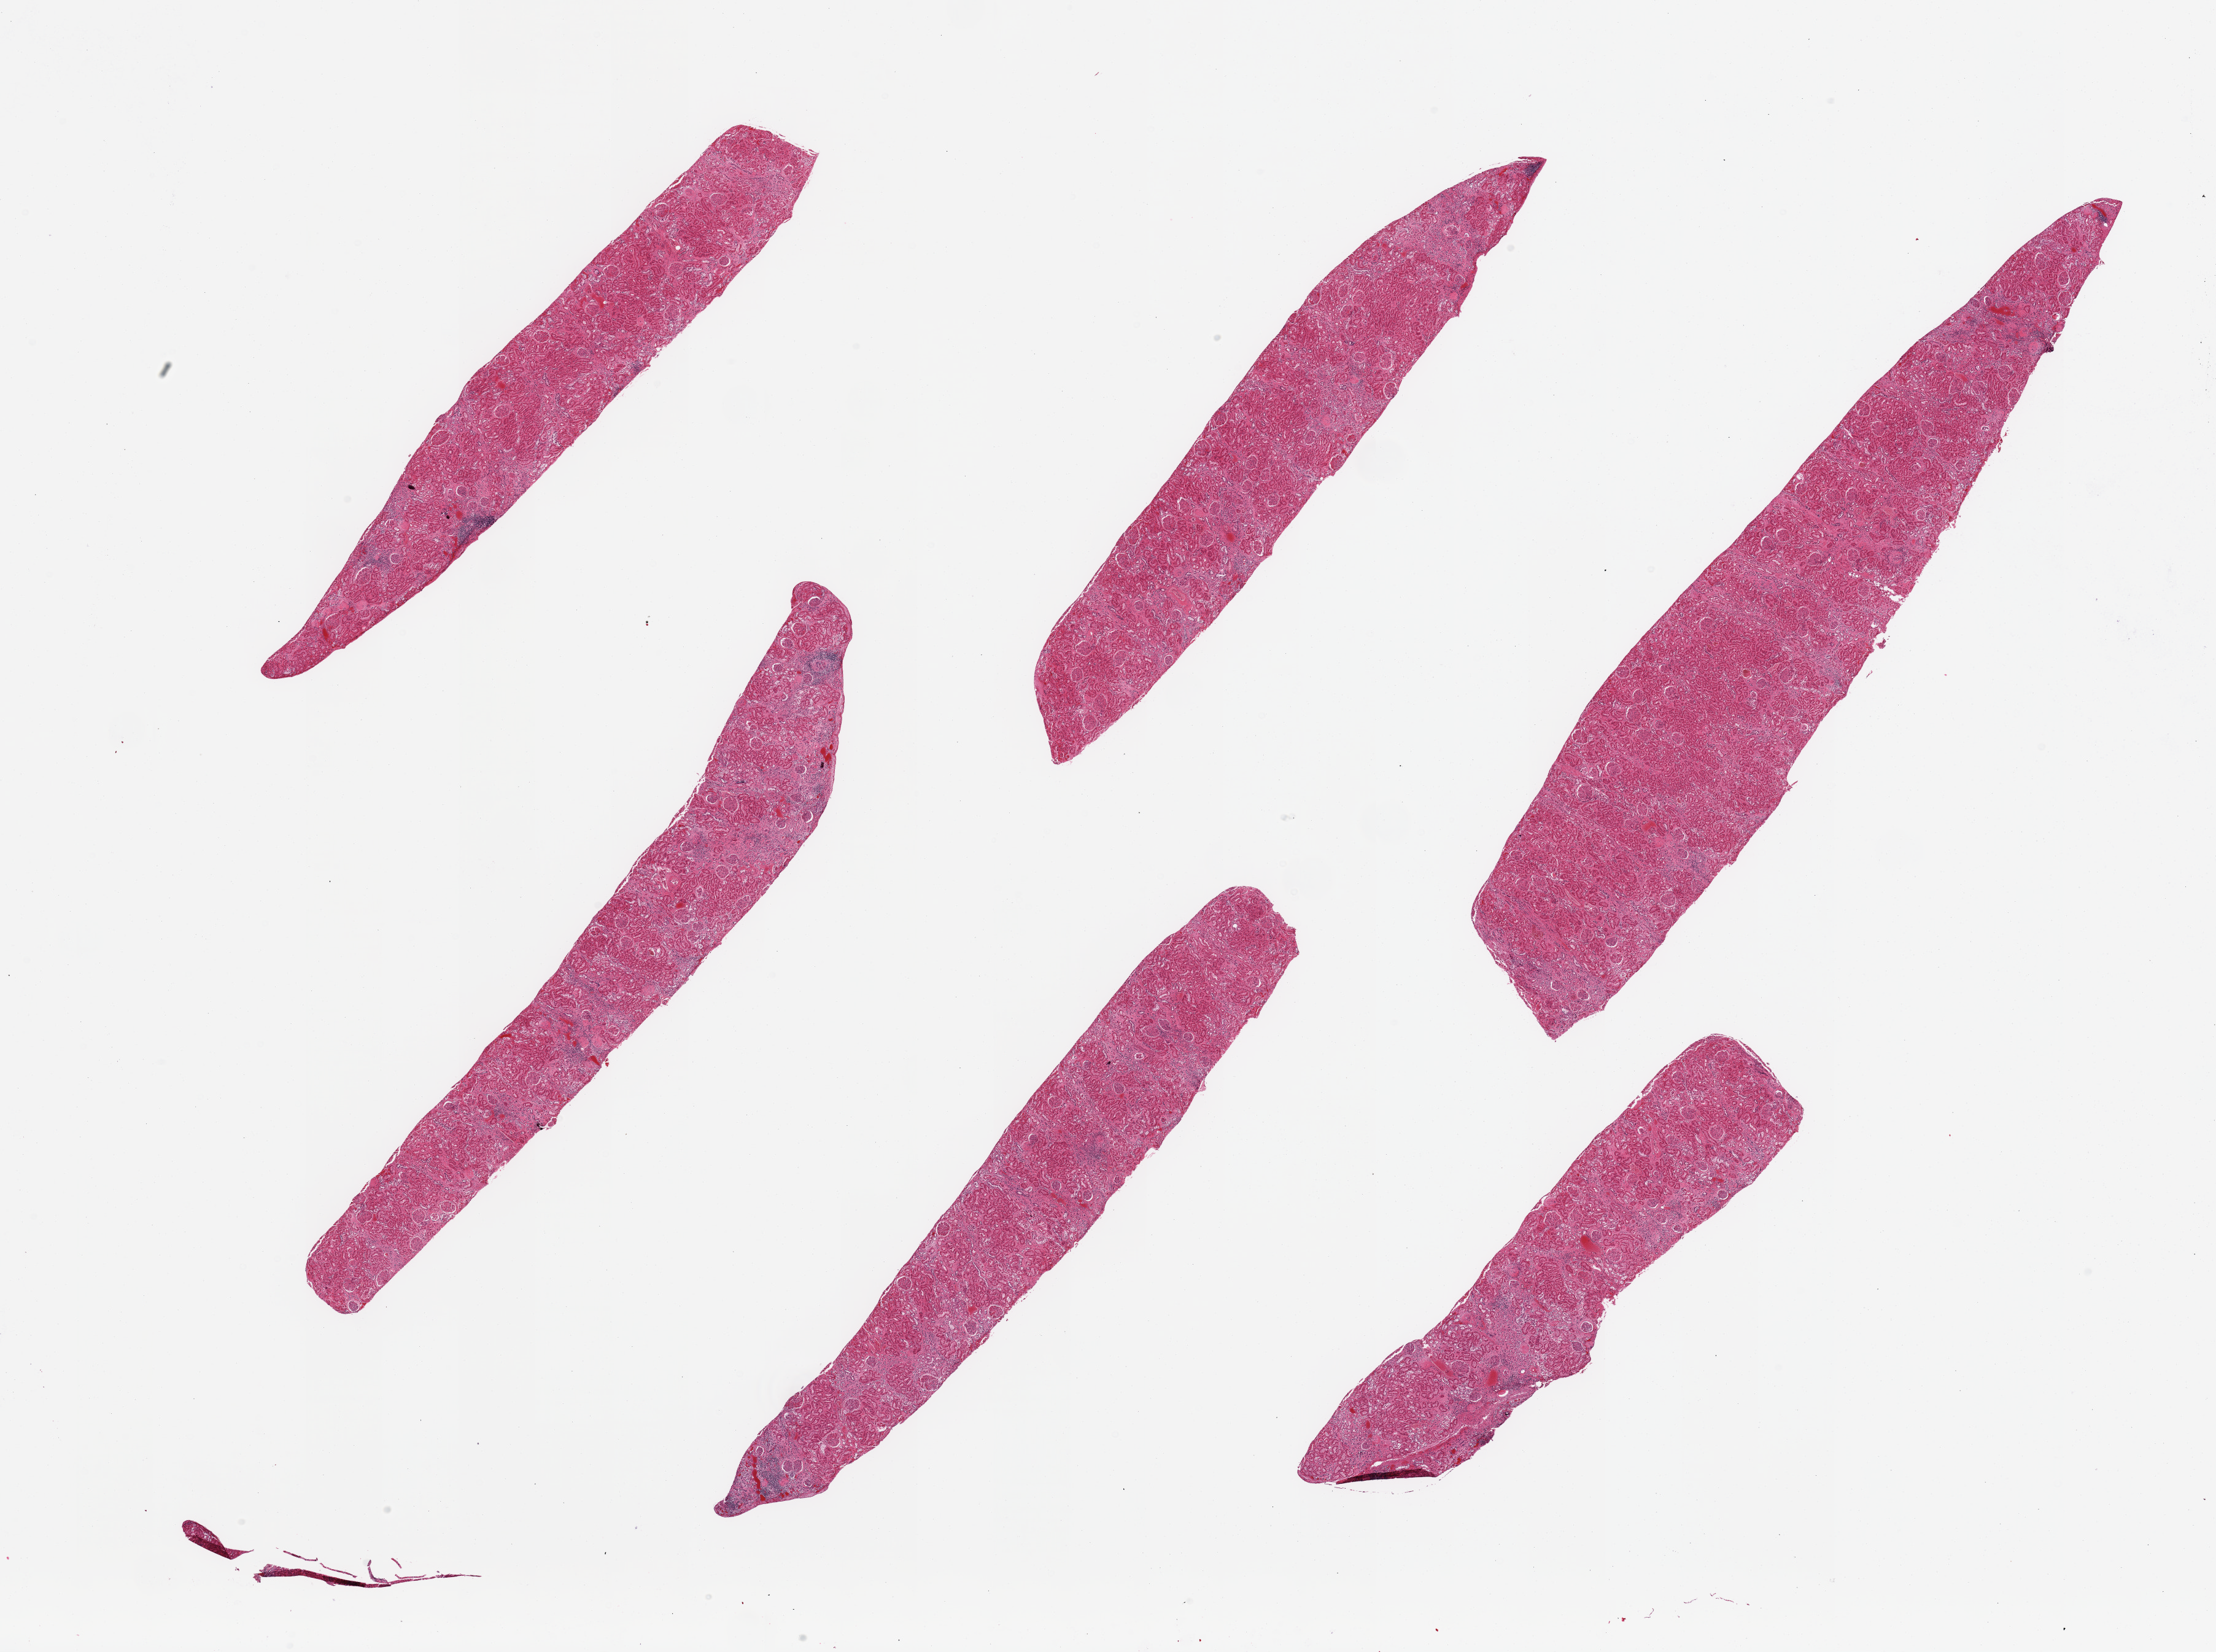
Digitized haematoxylin and eosin-stained section — whole scanned area (about 28.5 x 21.3 mm) shown as a low-resolution overview. PAXgene-fixed paraffin-embedded (PFPE) section. Sampled site (target tissue): renal cortex. Donor tissue sample. Donor sex: male.
Pathologist's review note for this sample: 6 pieces; mild to moderate cortical autolysis; arterio and arteriolonephrosclerosis with hyalinized glomeruli; interstitial fibrosis with scarring and lymphocytic infiltrates; scattered ductal calcifications; congestion.